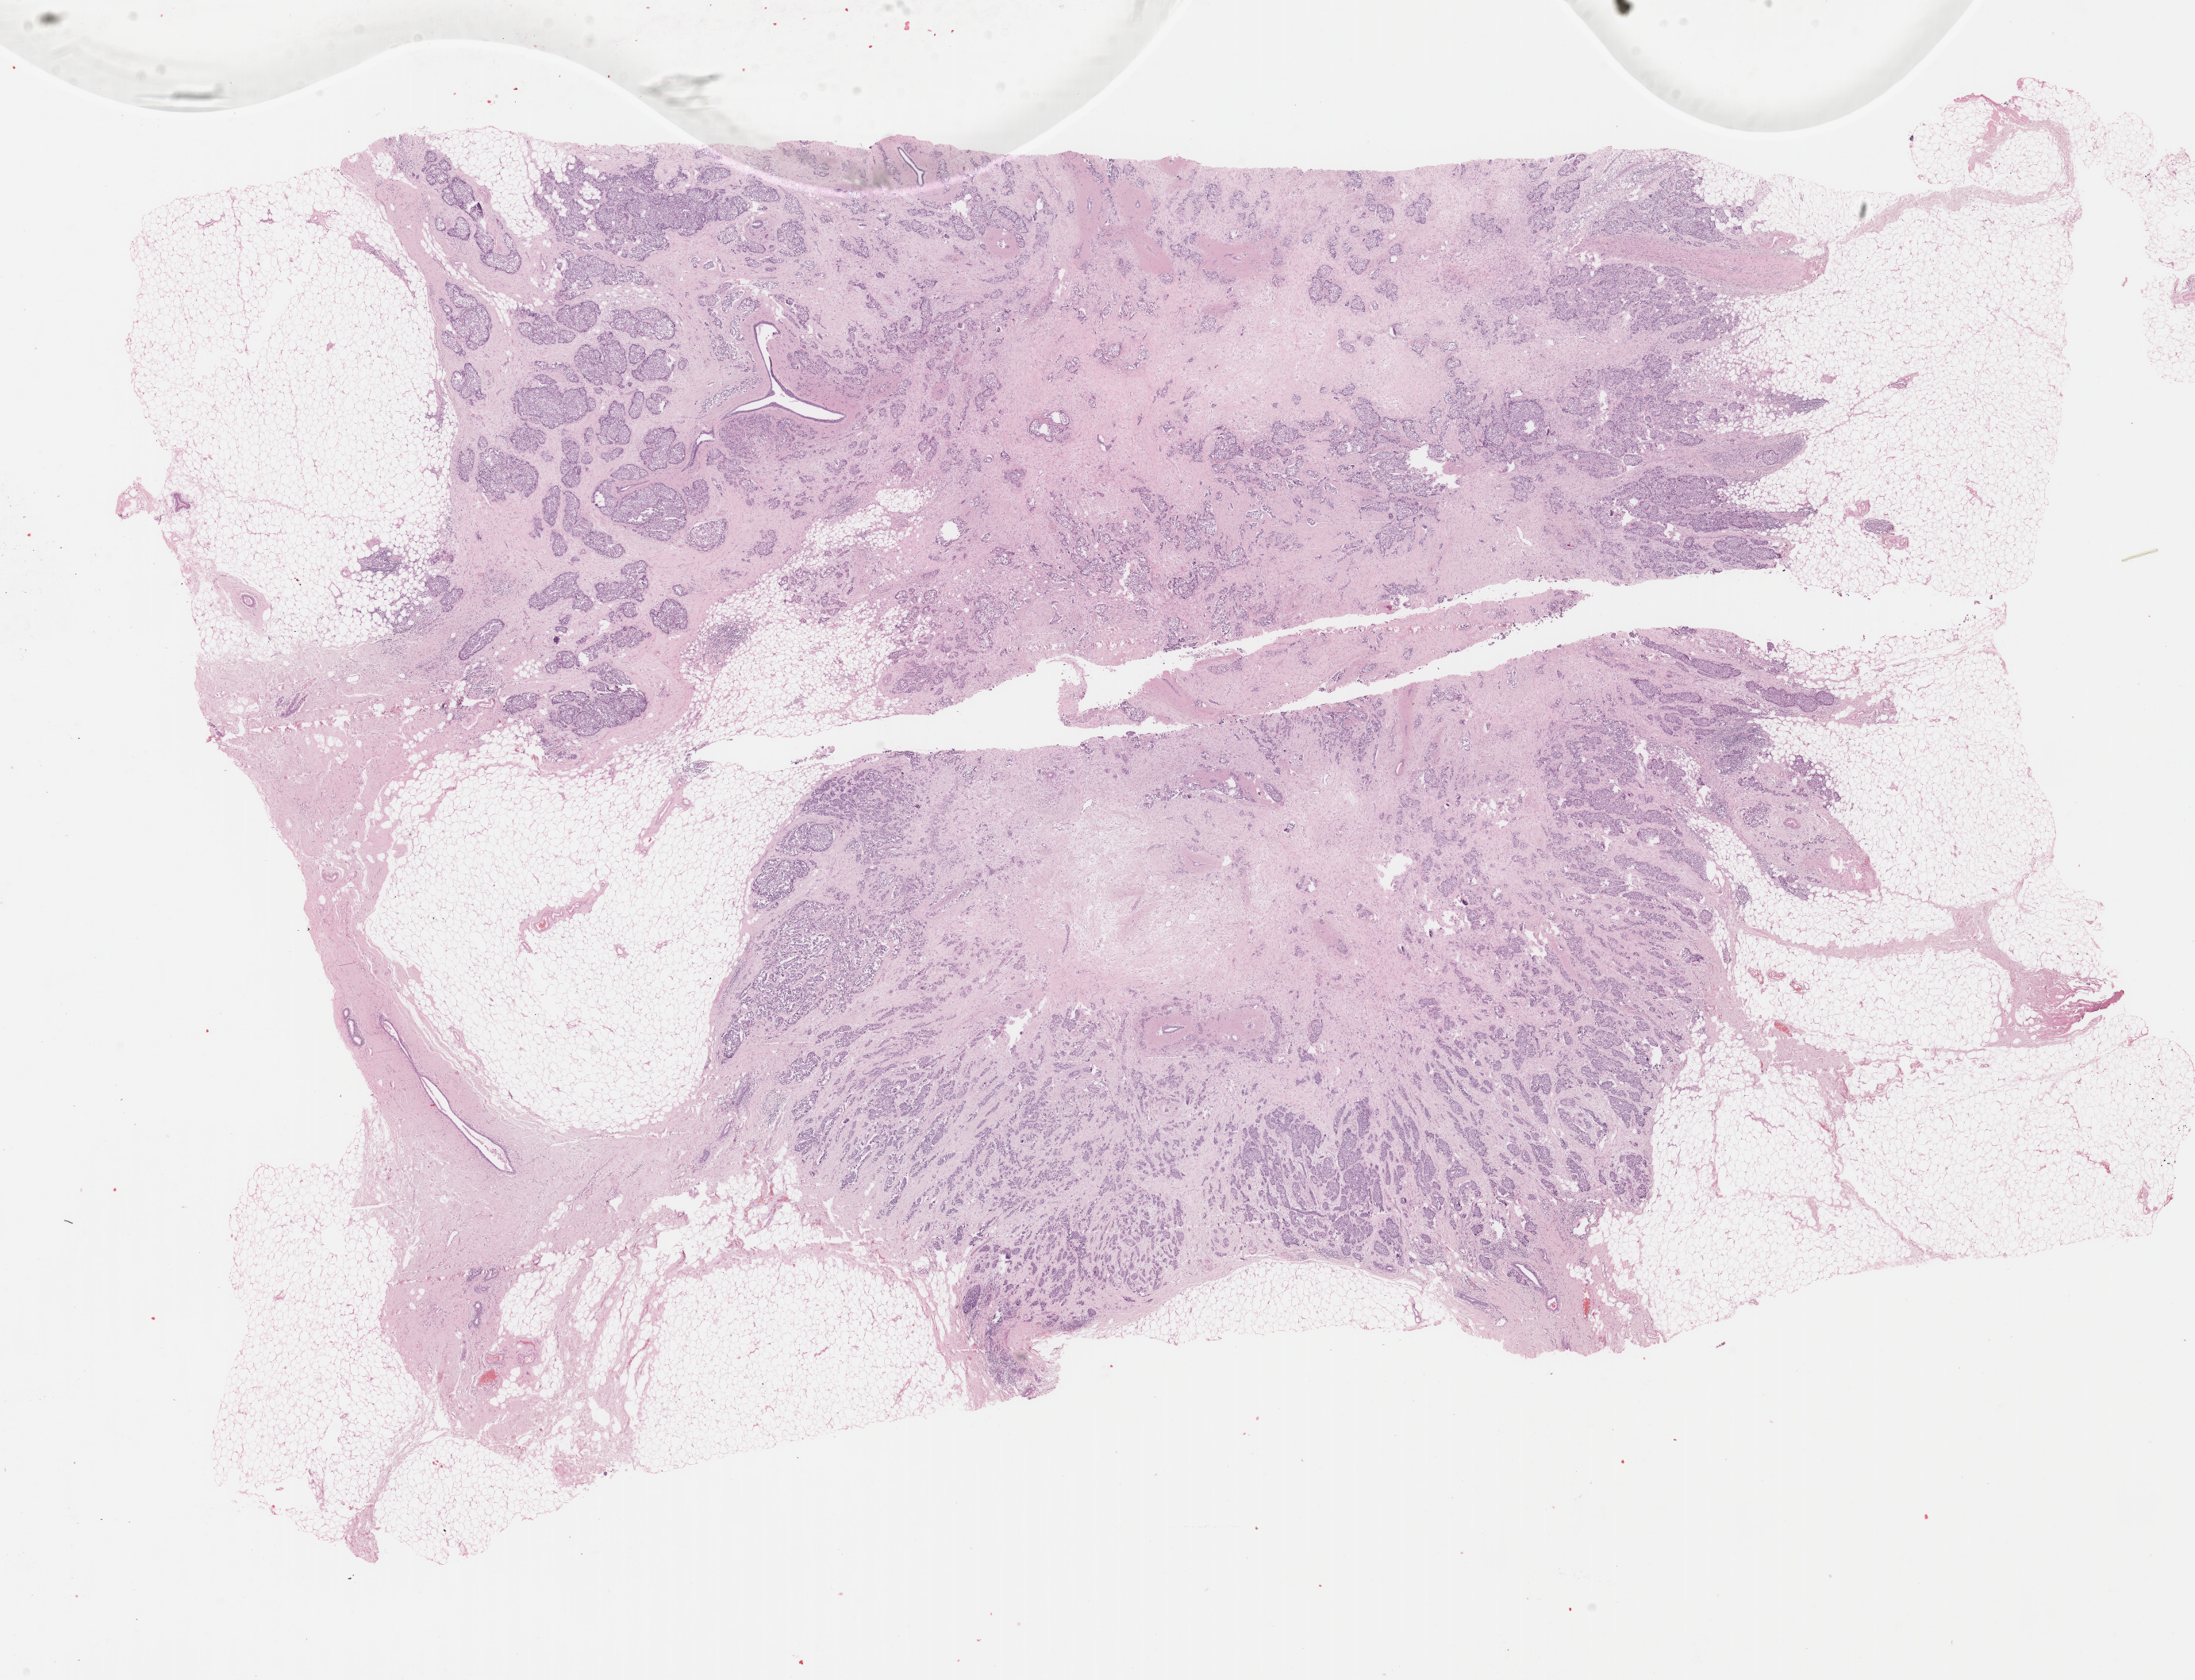
Whole-slide histology image, H&E-stained — a low-resolution overview of the entire scanned area, about 22.0 x 16.8 mm, formalin-fixed paraffin-embedded (FFPE) diagnostic section, breast, primary tumour sample. Female, age 73 years at initial diagnosis.
AJCC pathologic stage: IA (7th edition). Pathologic diagnosis: Infiltrating duct carcinoma, NOS.